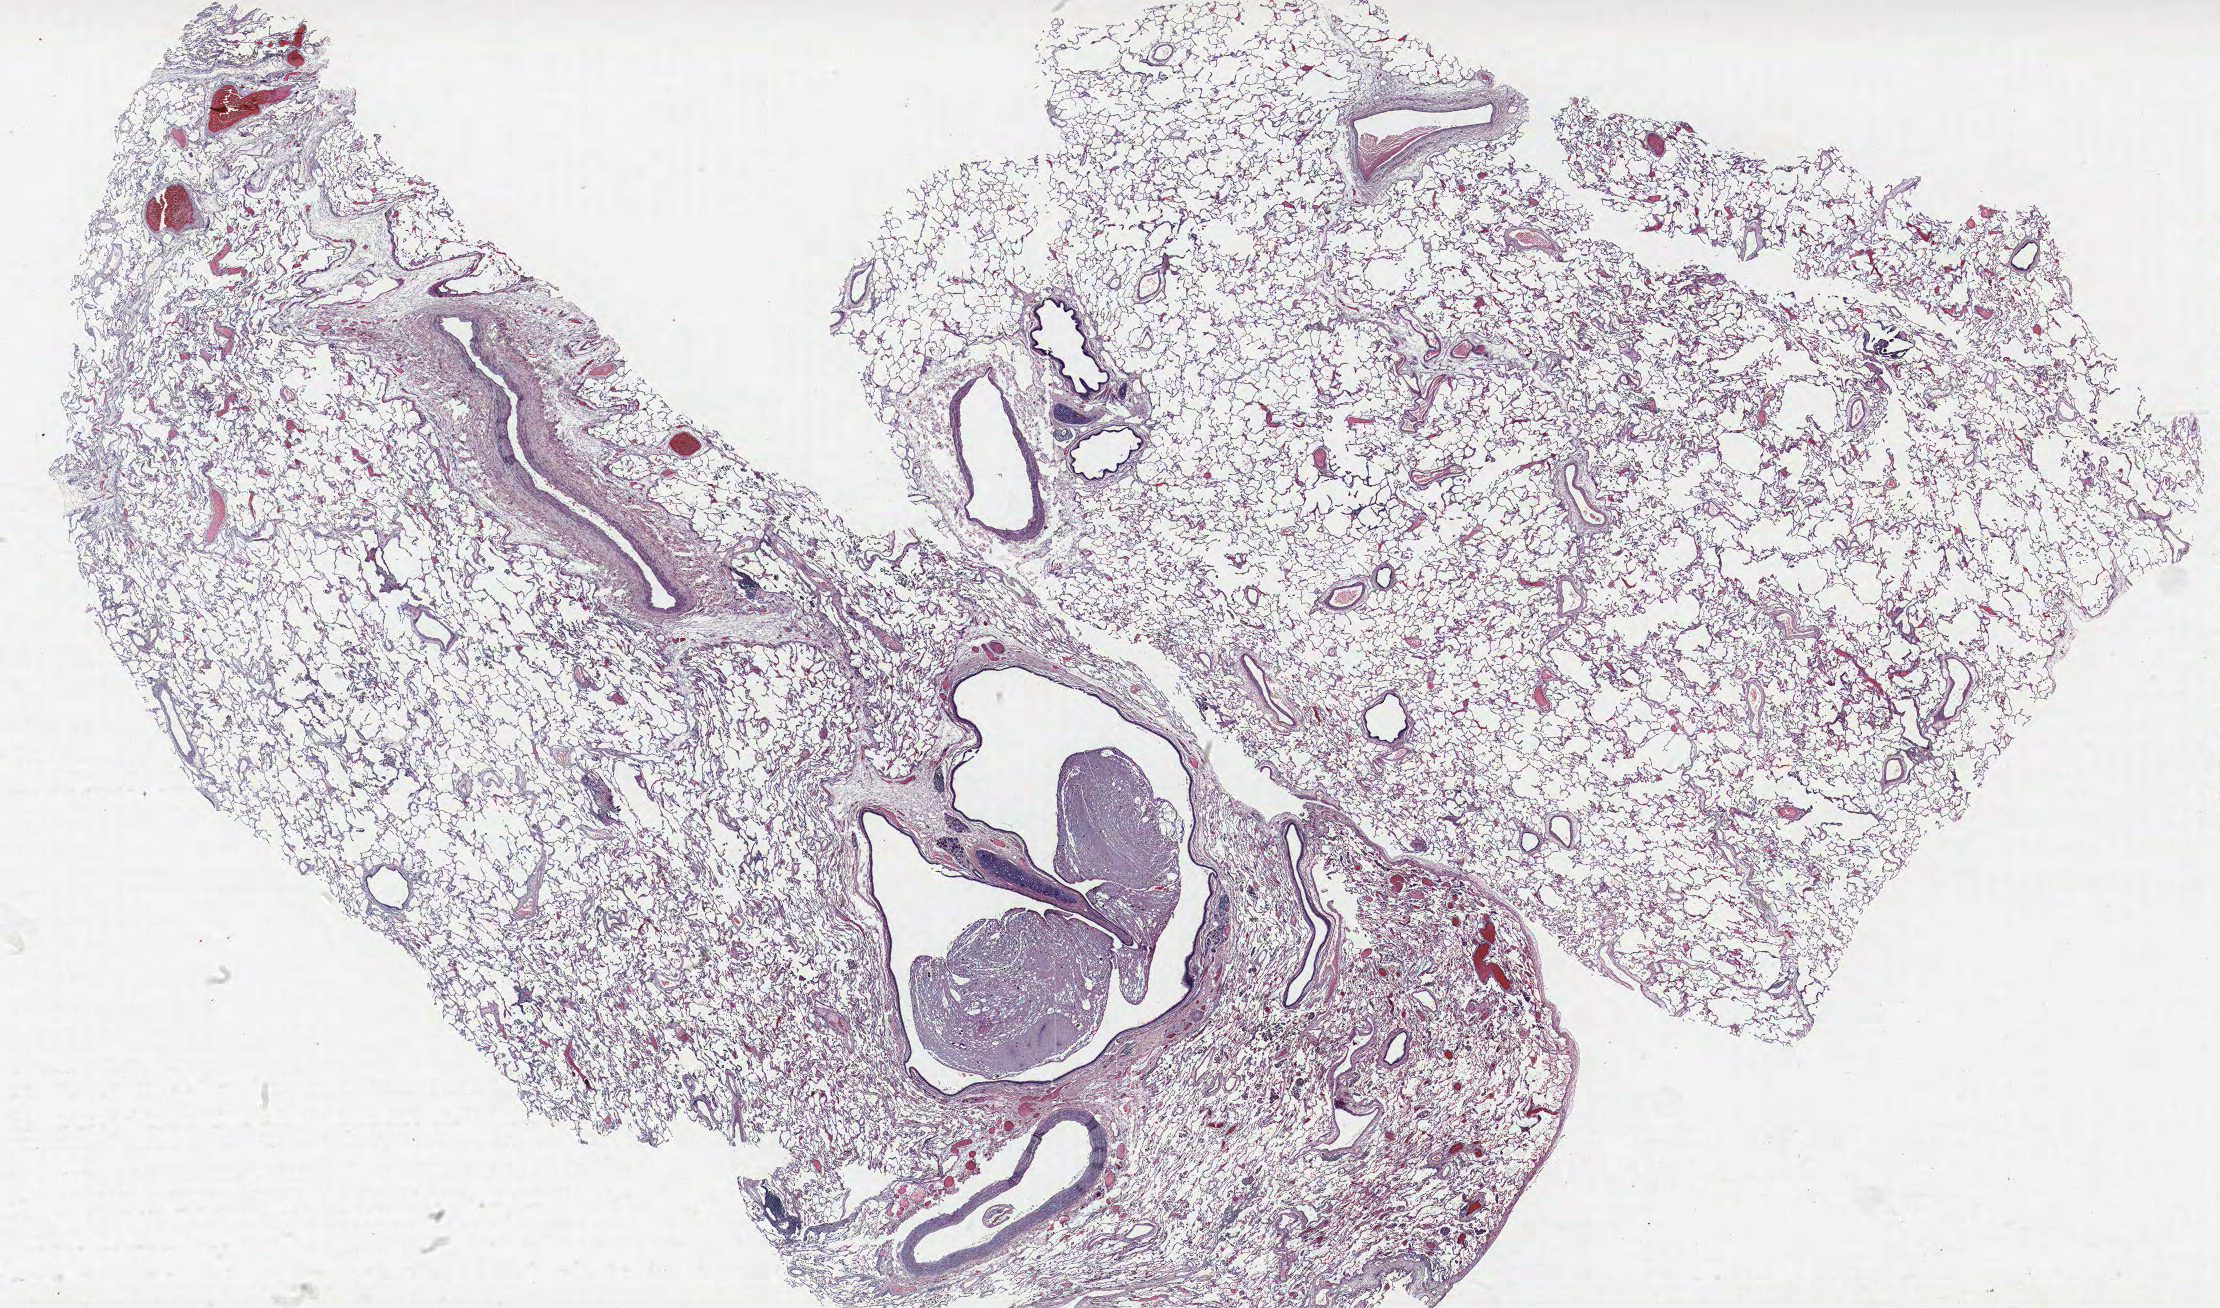
H&E-stained whole-slide image — whole scanned area (about 35.5 x 20.9 mm) shown as a low-resolution overview, formalin-fixed paraffin-embedded (FFPE) section, lung tissue. Female, age 60 at enrolment. Grade: moderately differentiated (G2).
* participant's lung-cancer diagnosis: Adenocarcinoma, NOS (ICD-O-3 8140/3)
* tumour size (pathology): 28 mm
* primary tumour location (clinical record): right lower lobe
* stage (AJCC 6th edition): IIIB